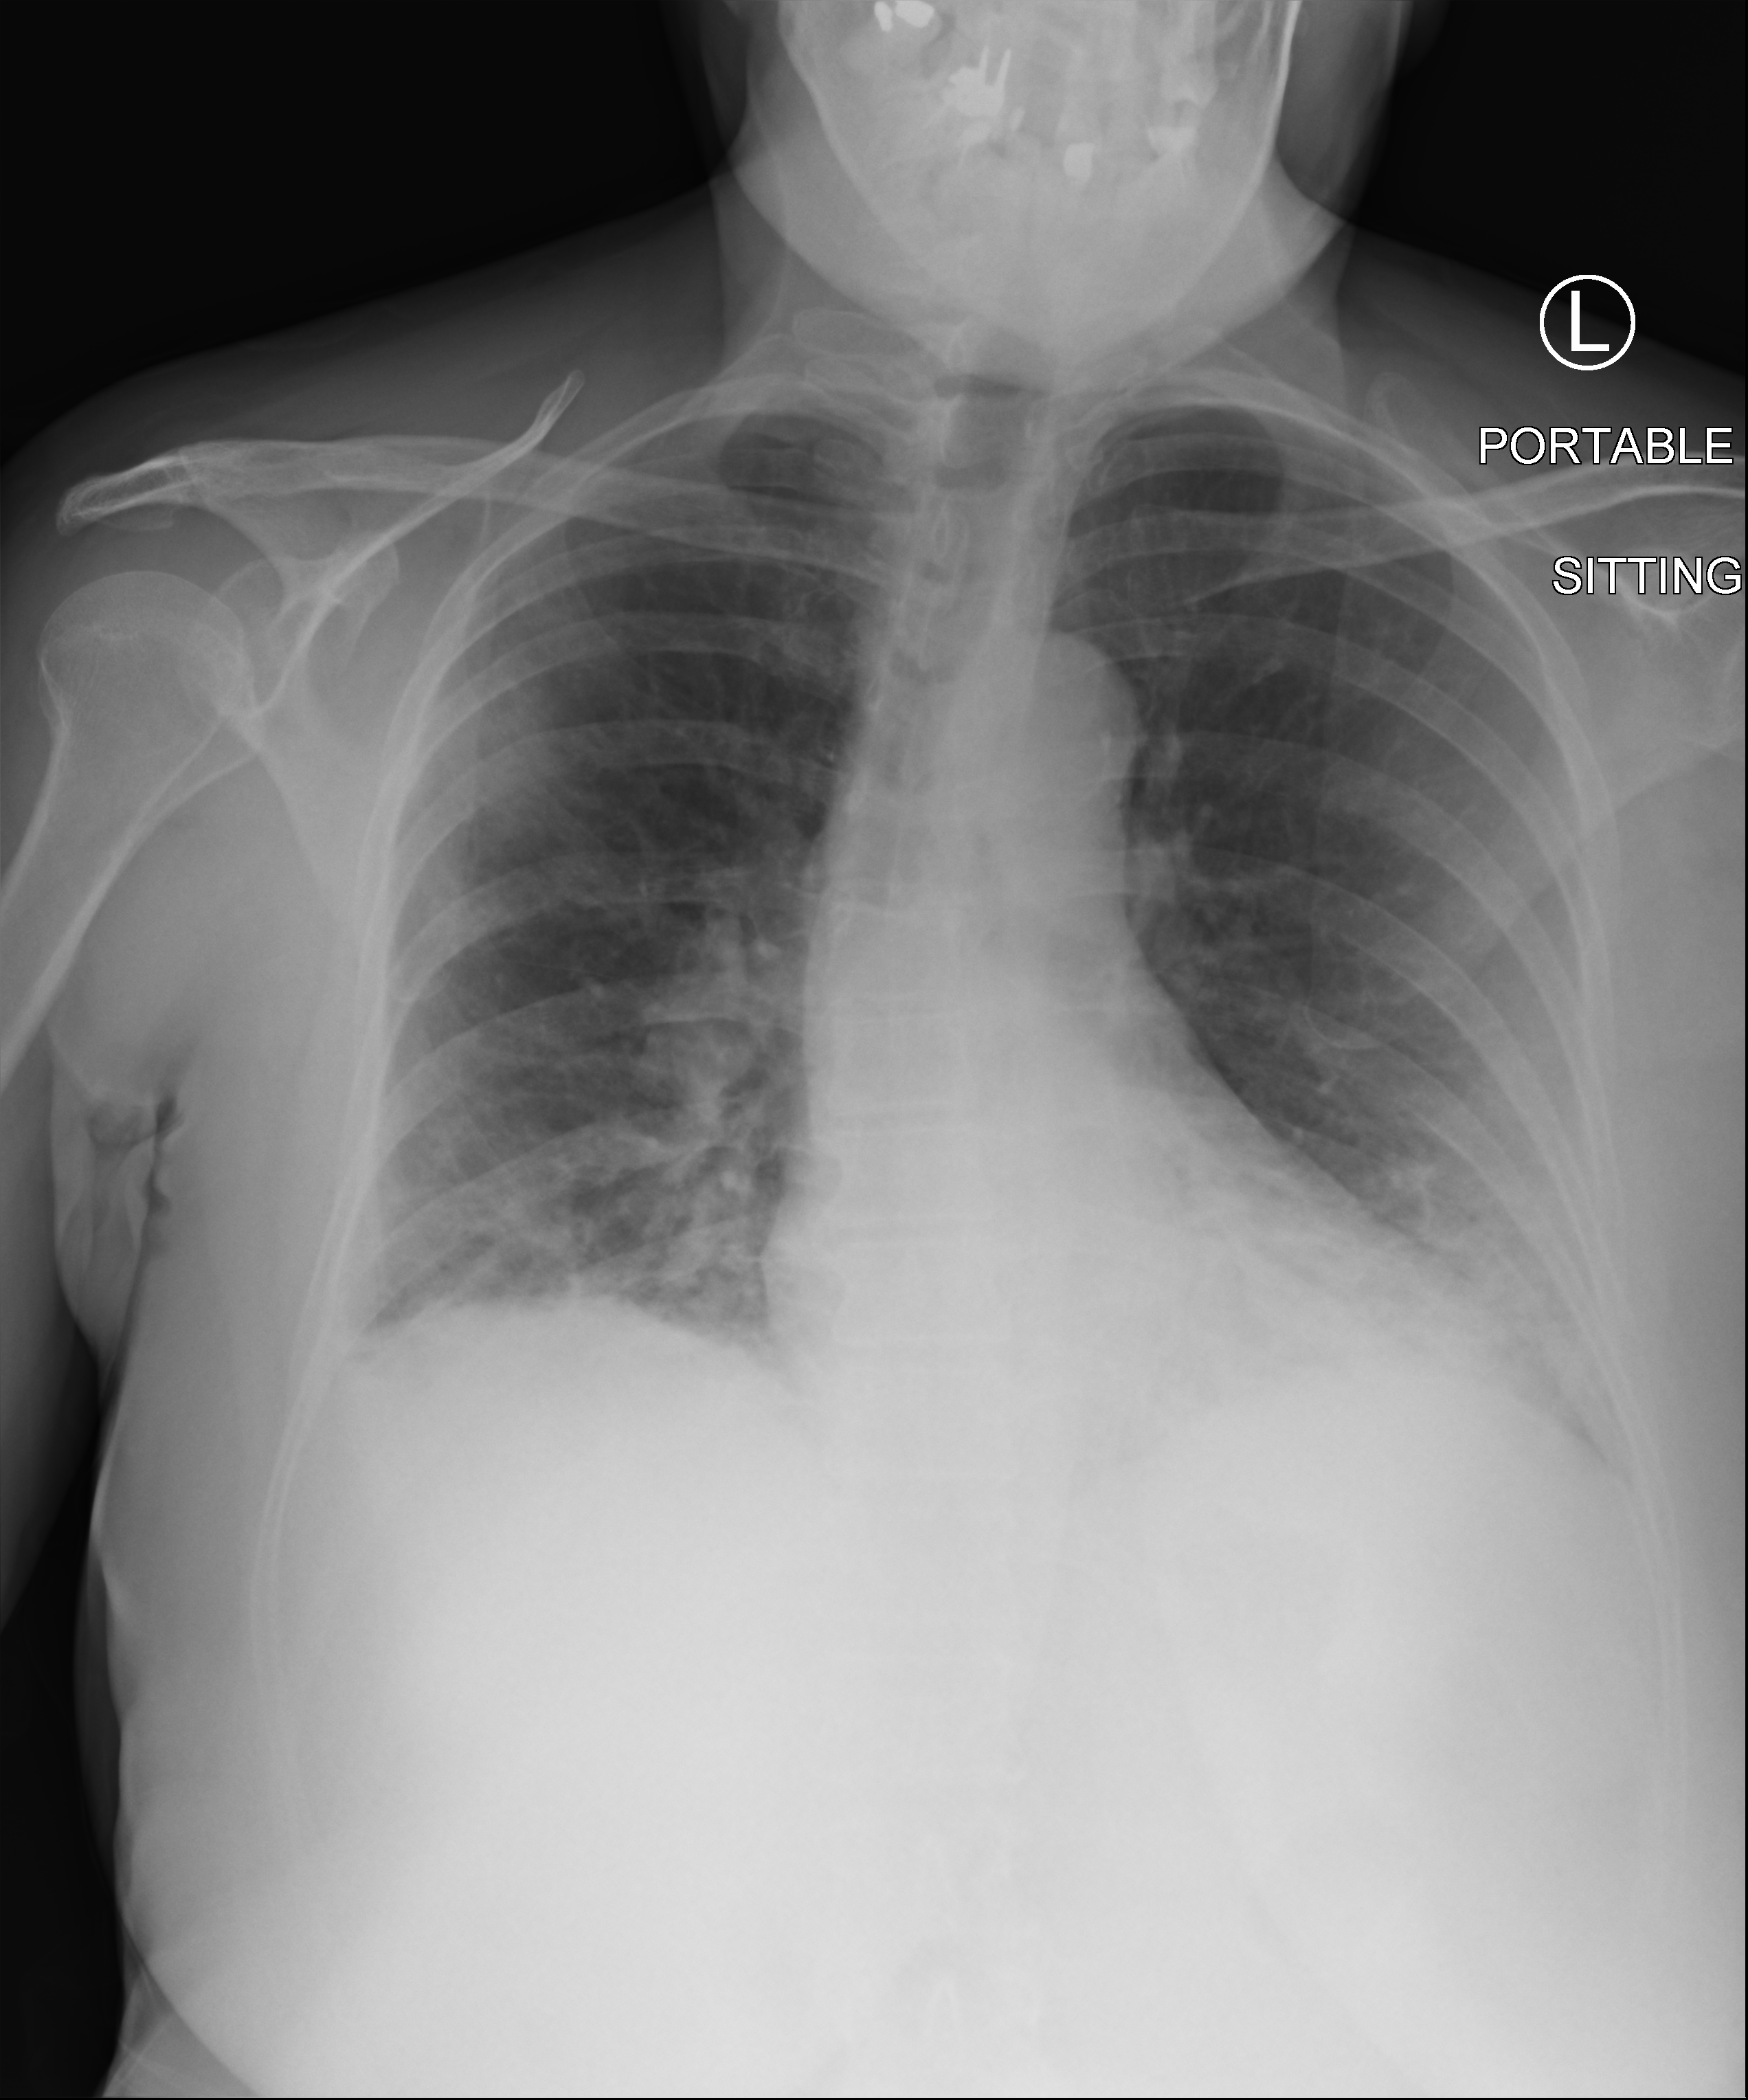
Portable chest radiograph; anteroposterior (AP) projection. Patient hospitalised with COVID-19; female, aged 60–74 years.
Hospital-stay facts (about this admission, not read from this image; timing relative to this image not recorded):
- mechanically ventilated during this hospital stay: no
- diabetes (admission record): no